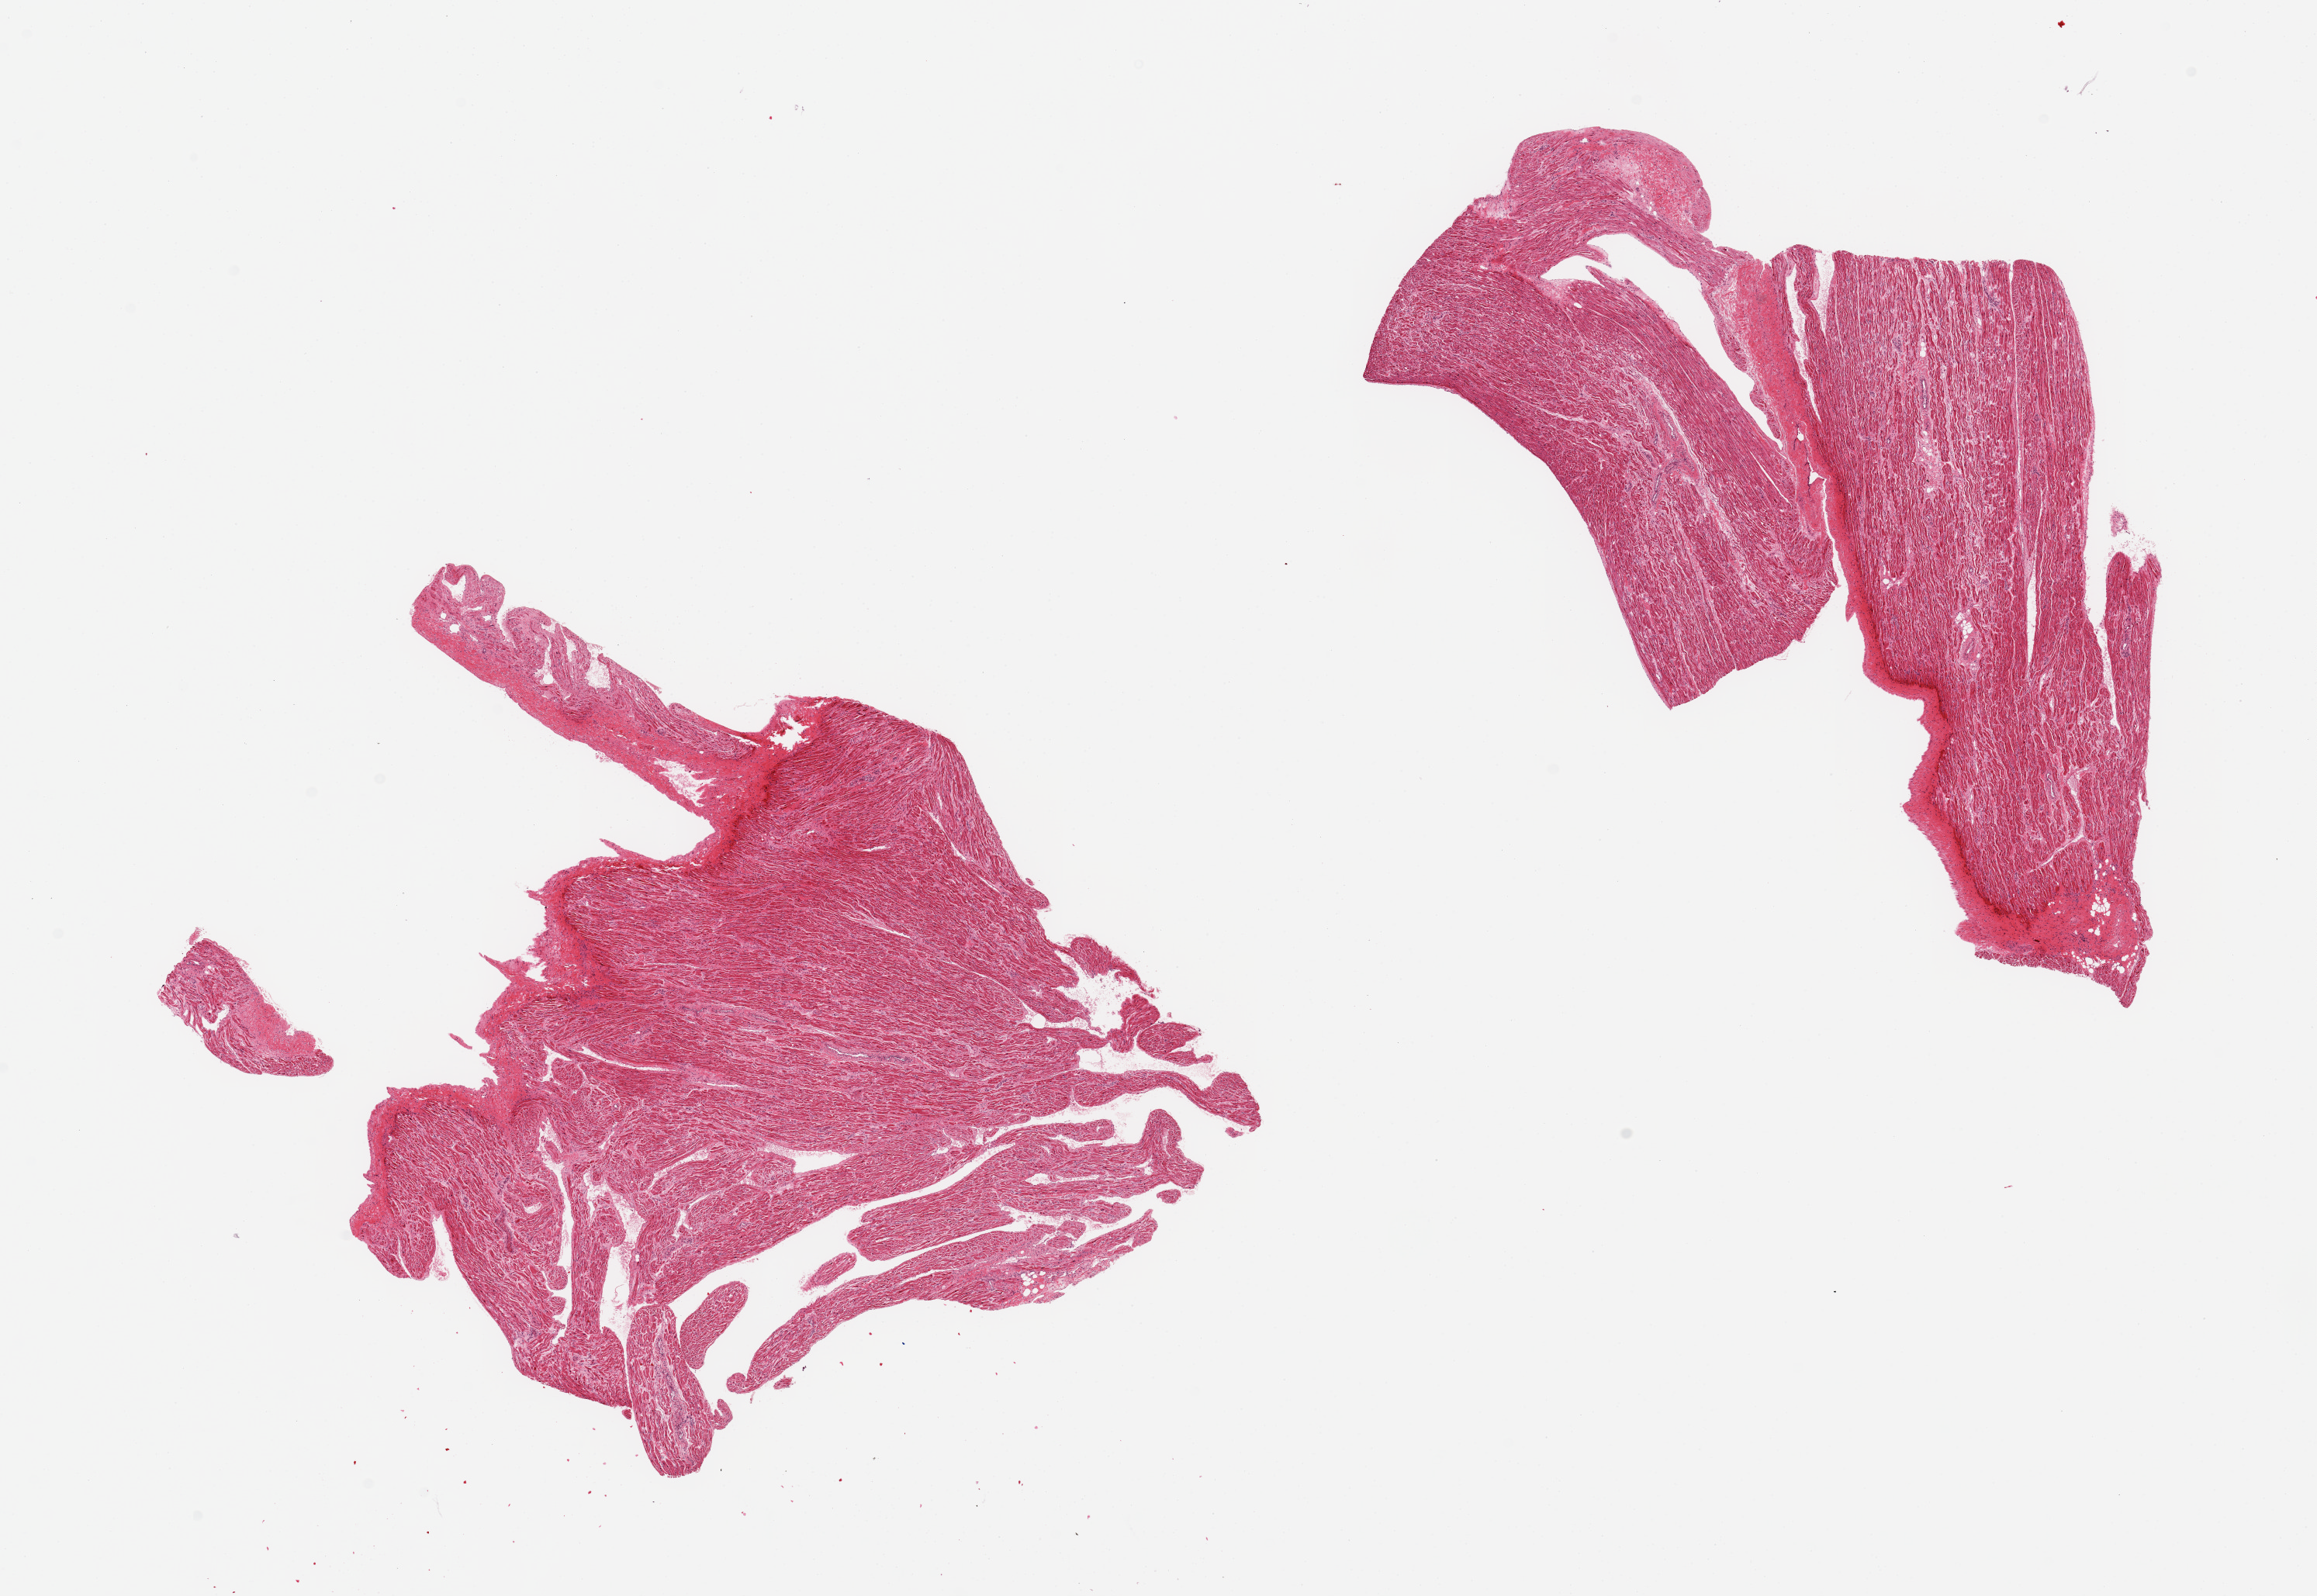
Whole-slide image, hematoxylin and eosin (H&E) stain, shown as a low-resolution overview of the whole scanned area (about 23.6 x 16.3 mm). PAXgene-fixed paraffin-embedded (PFPE) section. Sampled site (target tissue): auricular appendage. Tissue donor sample.
Pathologist's review note for this sample: 2 pieces.